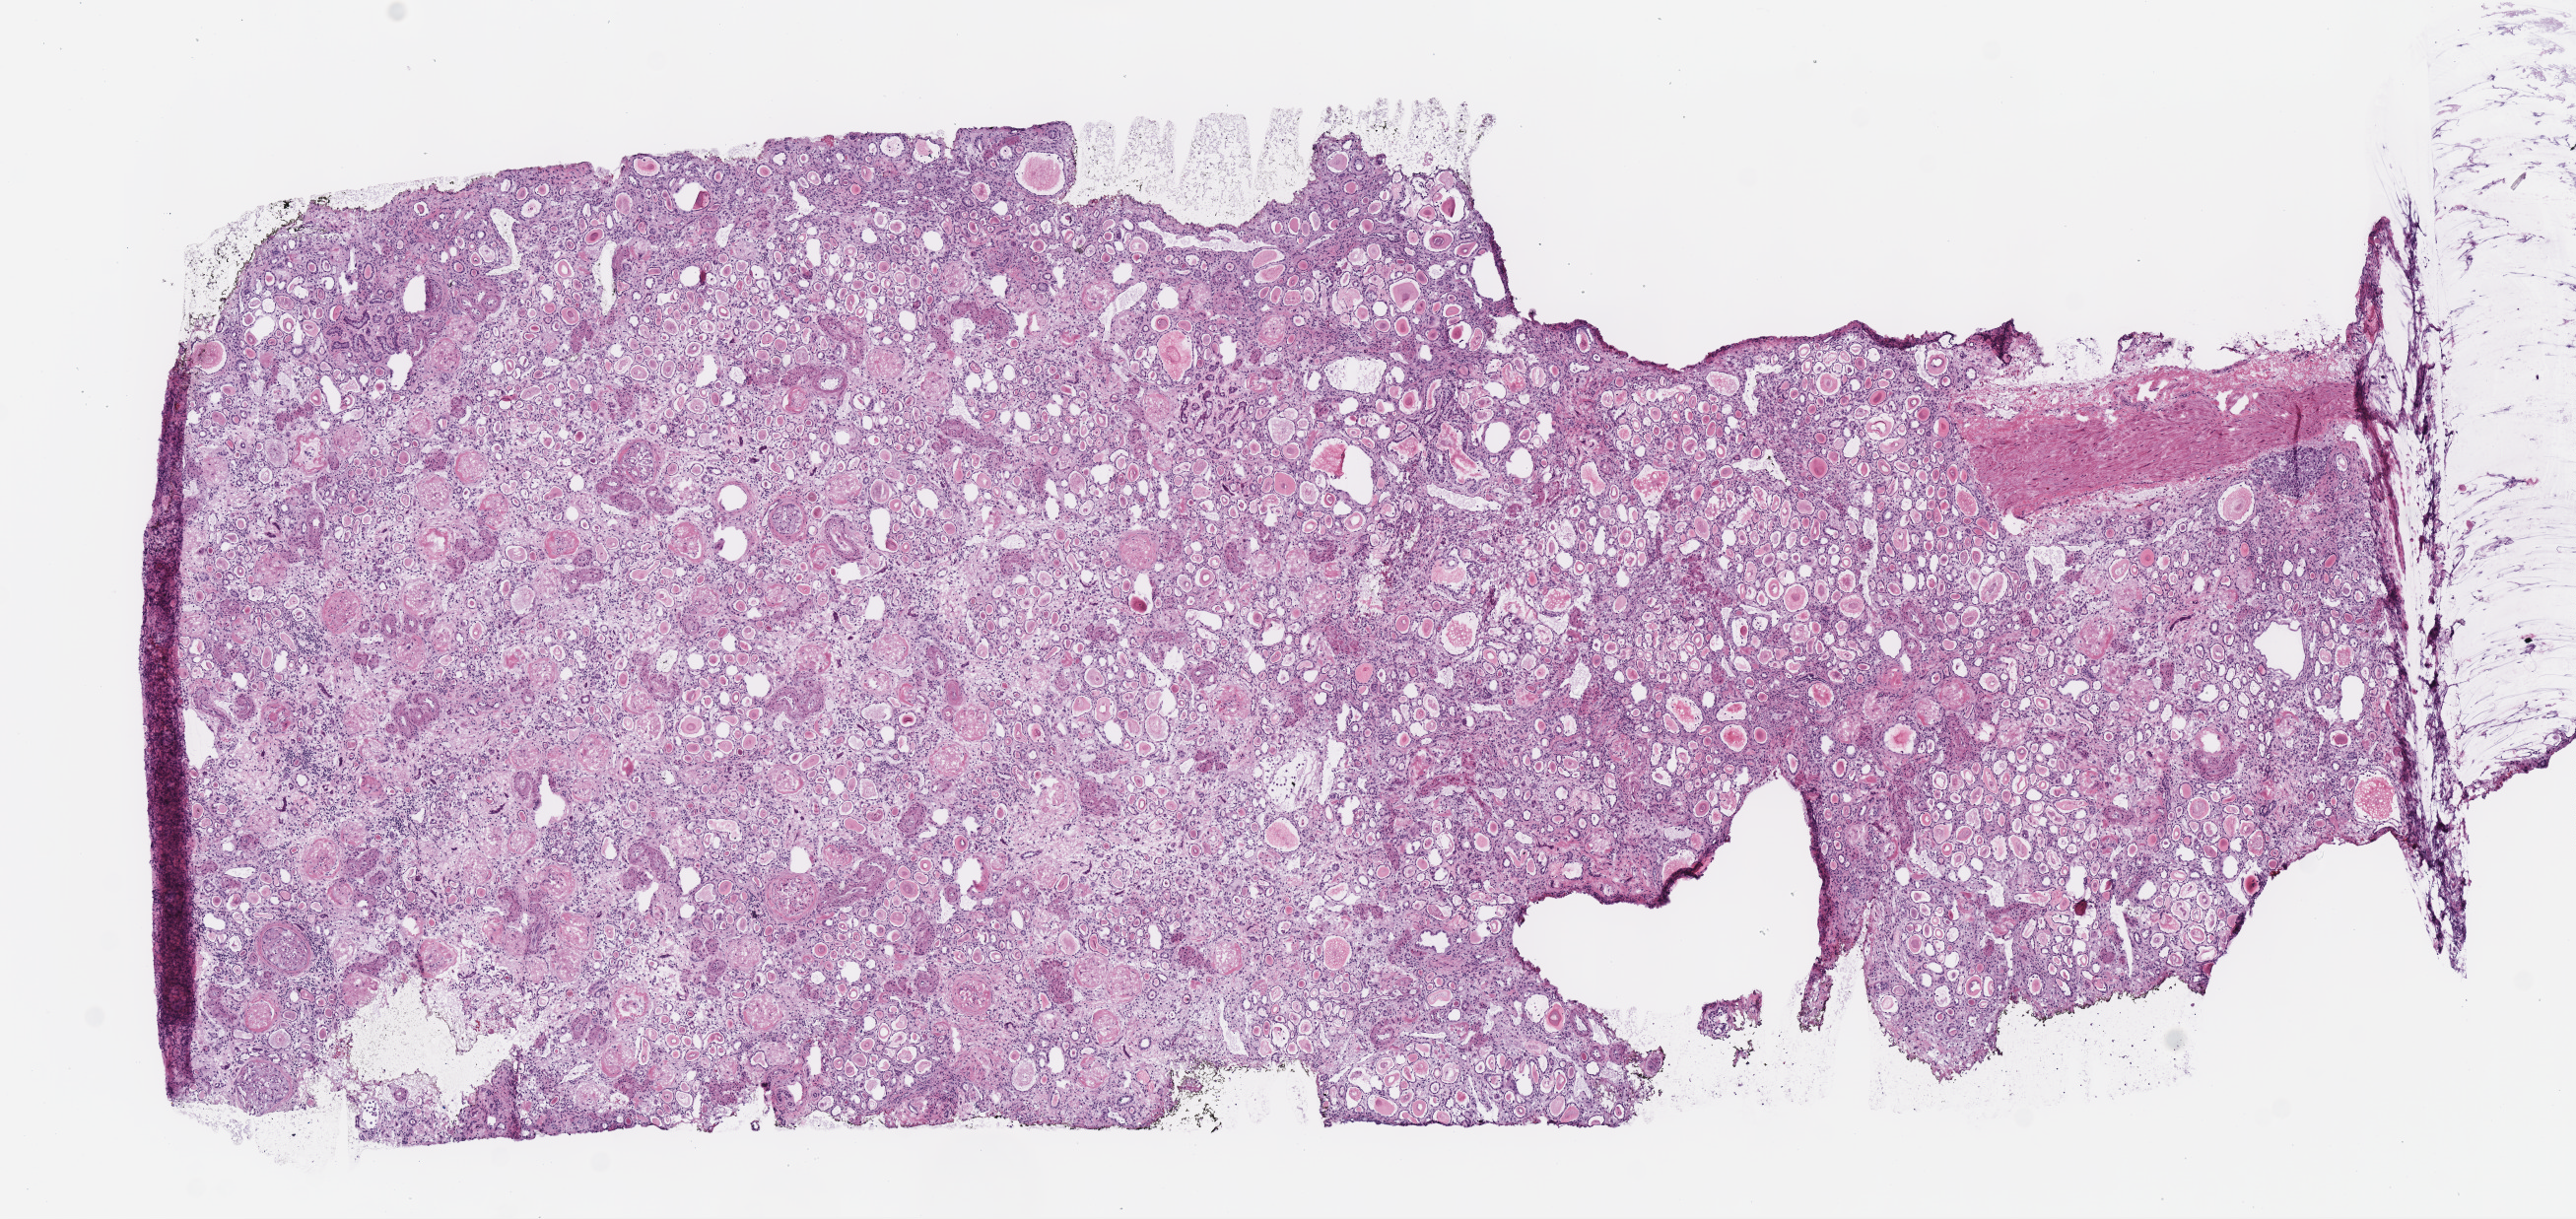
H&E-stained whole-slide image, shown as a low-resolution overview of the whole scanned area (about 10.3 x 4.9 mm). Frozen section from the top of the tissue portion. Kidney, solid tissue normal (non-tumour tissue) sample. Male patient; age at initial diagnosis 47 years.
• this section: solid tissue normal sample (biorepository sample class)
• patient diagnosis: Papillary adenocarcinoma, NOS